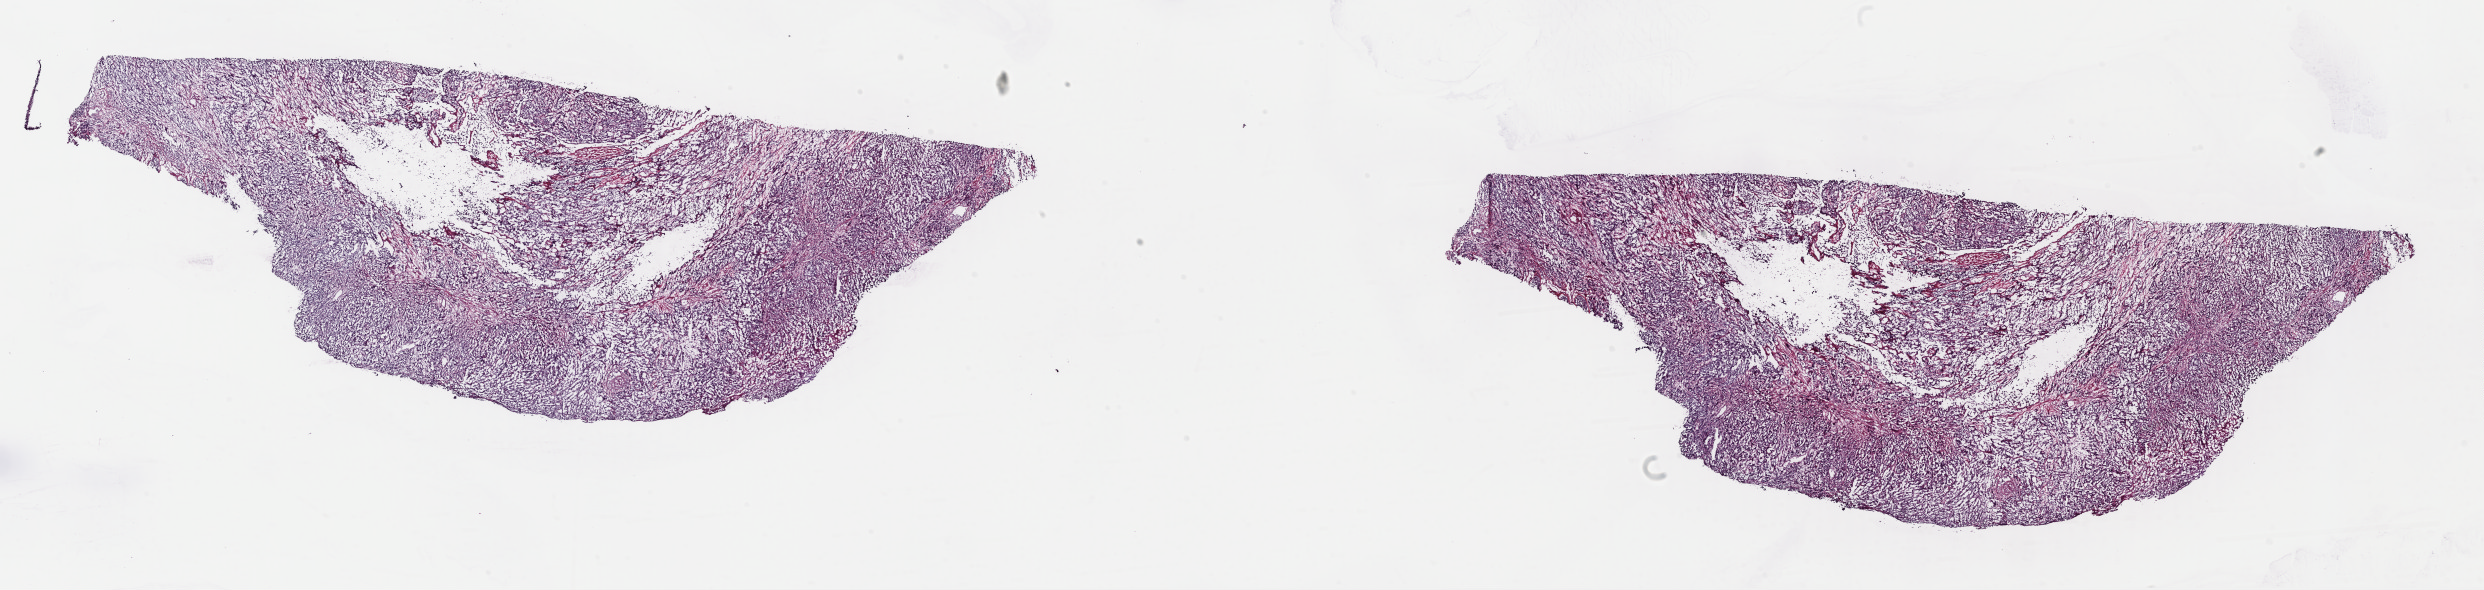
Whole-slide histology image, Hematoxylin and eosin (H&E) stained — a low-resolution overview of the entire scanned area, about 39.0 x 9.3 mm (from a 40x scan); frozen section from the top of the tissue portion; primary tumour sample from the bladder. Female, age 47 years at initial diagnosis. Histologic grade: high grade. Composition of this section per pathologist review: tumour cells 70%, tumour nuclei 70%, normal cells 0%, stromal cells 30%, necrosis 0%. Infiltration values recorded for this section: lymphocyte infiltration 4%, monocyte infiltration 2%, neutrophil infiltration 3%.
Lymph nodes positive (case pathology): 0 of 25 examined. Histologic diagnosis: Transitional cell carcinoma. AJCC pathologic stage: III (7th edition).